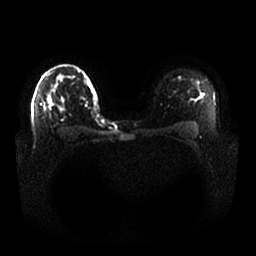
Breast MRI, one axial slice. Position 18 of 25 along the scan axis. Diffusion-weighted series; image 2 of 4 stored at this slice position (different b-values; order by instance number). 1.5 T. 256 × 256 image matrix, field of view 370 × 370 mm. Female patient.
Structures marked on this image (outlined manually by an expert reader):
- tumour on diffusion-weighted imaging: bounding box <49,98,52,105> (left, top, right, bottom; pixels)